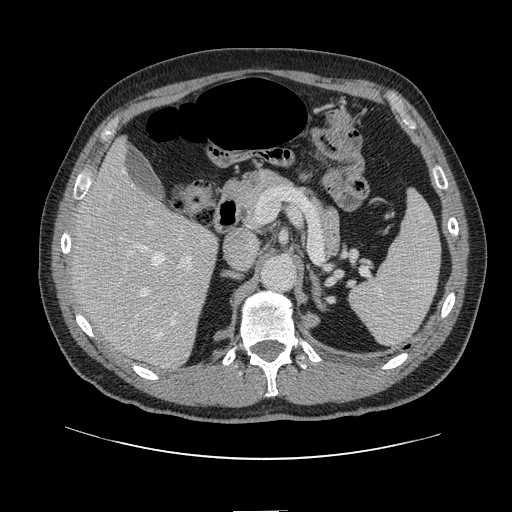
Contrast-enhanced abdominal CT, one axial slice. Slice 76 of 161 in the series (ordered by position). 120 kVp. Soft-tissue window (W 400 / L 40 HU). 512 × 512 image matrix, field of view 412 × 412 mm. Male patient, age 66 years. Case-level facts recorded for this patient, not image findings: diagnosis: colorectal cancer liver metastases, imaged before liver resection; multiple liver metastases: no; largest metastasis: 3.5 cm; disease in both lobes: no.
Outlined on this slice (outlined manually by an expert reader):
- hepatic veins: bounding box <122,169,175,324> (left, top, right, bottom; pixels)
- liver: <75,143,216,368>
- planned liver remnant (the part of the liver to remain after resection): <75,143,199,294>
- portal vein (with intrahepatic branches): <123,221,193,314>